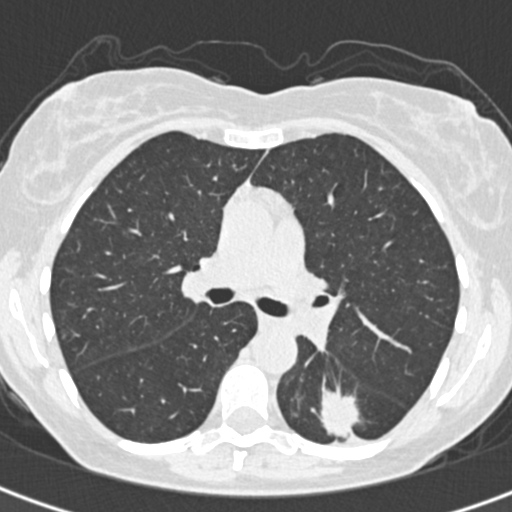
Low-dose screening chest CT, one axial slice; position 205 of 328 along the scan axis; reconstruction kernel B30f; lung window (W 1500 / L -600 HU); 512 × 512 image matrix, field of view 284 × 284 mm.
Structures marked on this image (expert manual segmentation):
- lesion 1 (tumor, lower lobe of left lung): bounding box <319,388,360,436> (left, top, right, bottom; pixels)